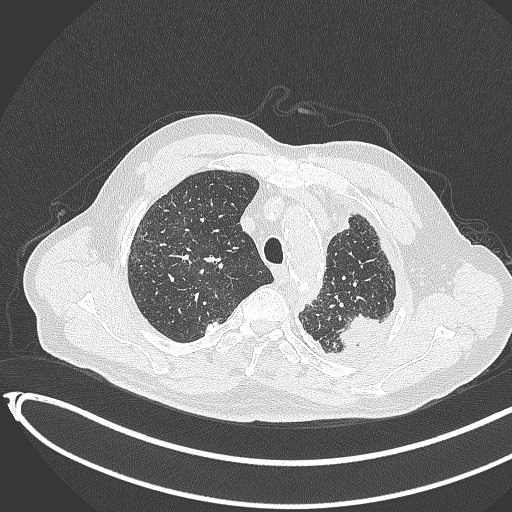
Chest CT, one axial slice. Slice 346 of 451 in the series (ordered by position). Lung window (W 1500 / L -600 HU). 1 mm slice thickness. 512 × 512 image matrix. Male patient, age 78 years. From the clinical record (not read from this slice): clinical TNM (as recorded): T1c N0 M1.
Annotated regions visible in this slice (bounding box drawn by a radiologist):
- lung tumour (recorded histology: adenocarcinoma): bounding box <338,308,382,347> (left, top, right, bottom; pixels)